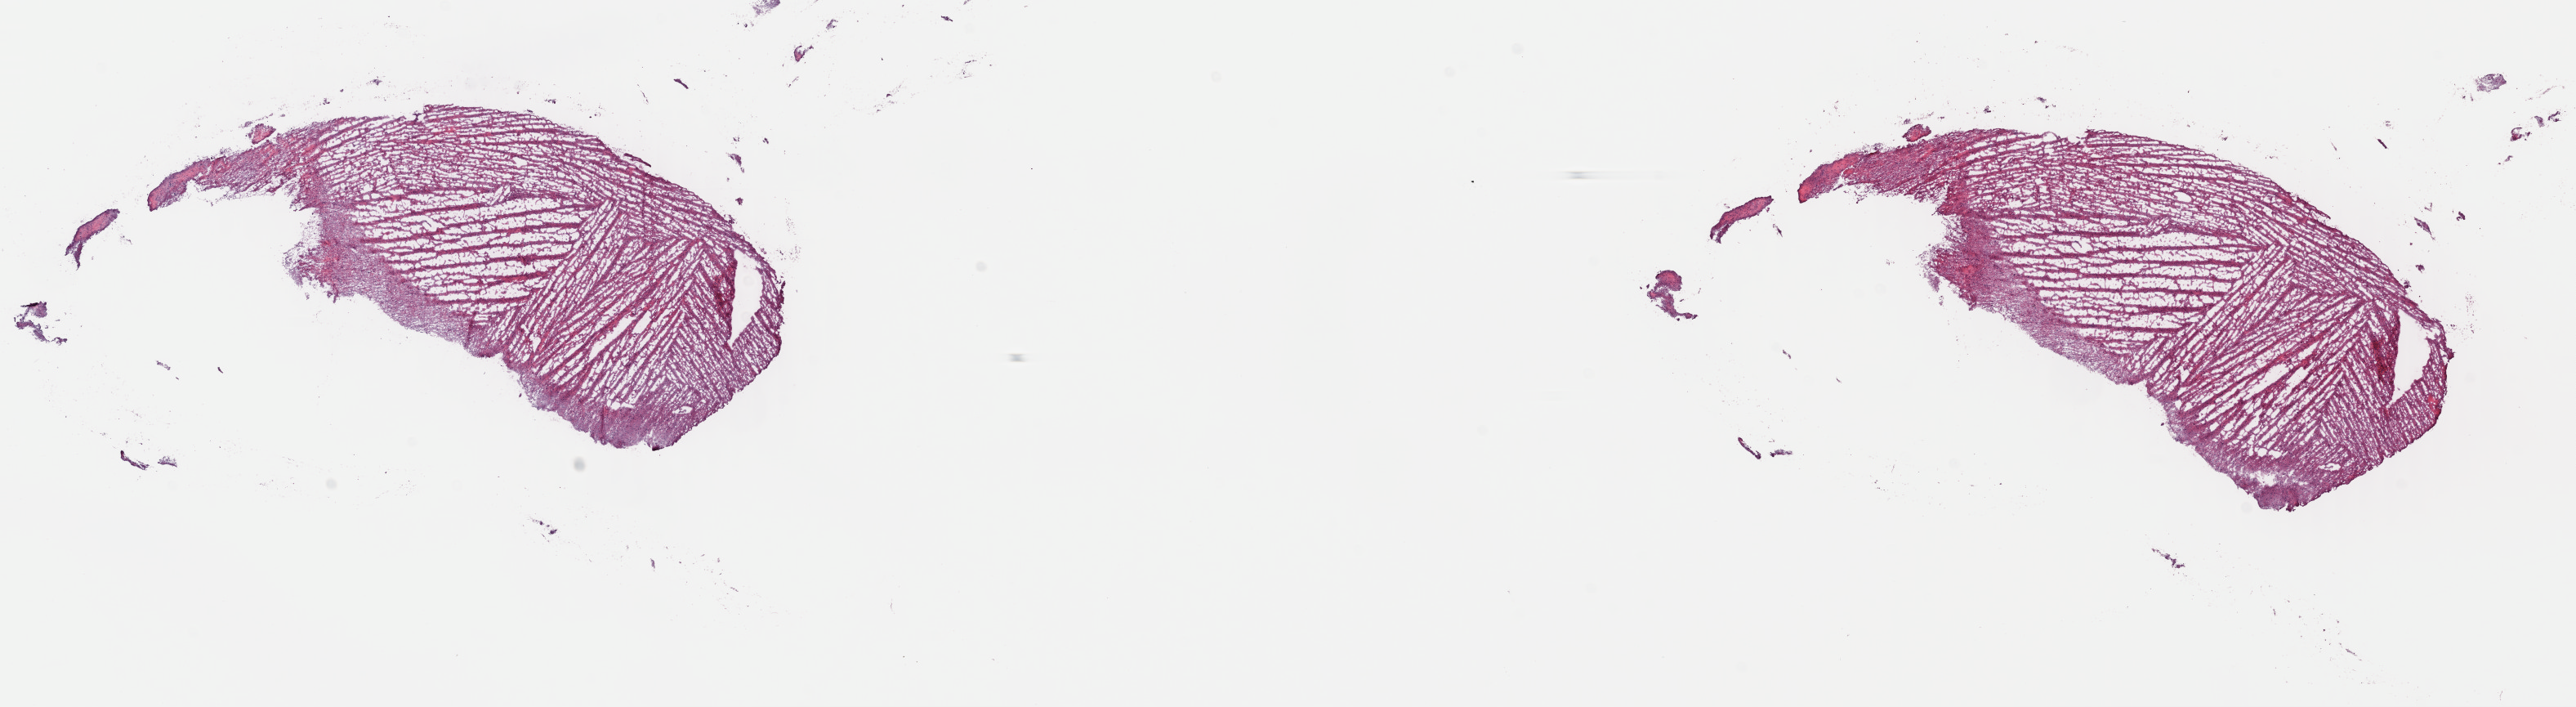
H&E whole-slide image, a low-resolution overview of the entire scanned area, about 24.8 x 6.8 mm (from a 40x scan), frozen section, sample: primary tumour, brain. Female, age 52 years at initial diagnosis. Slide review estimates, as recorded: tumour cells 30%, tumour nuclei 80%.
Histologic diagnosis: Oligodendroglioma, anaplastic.